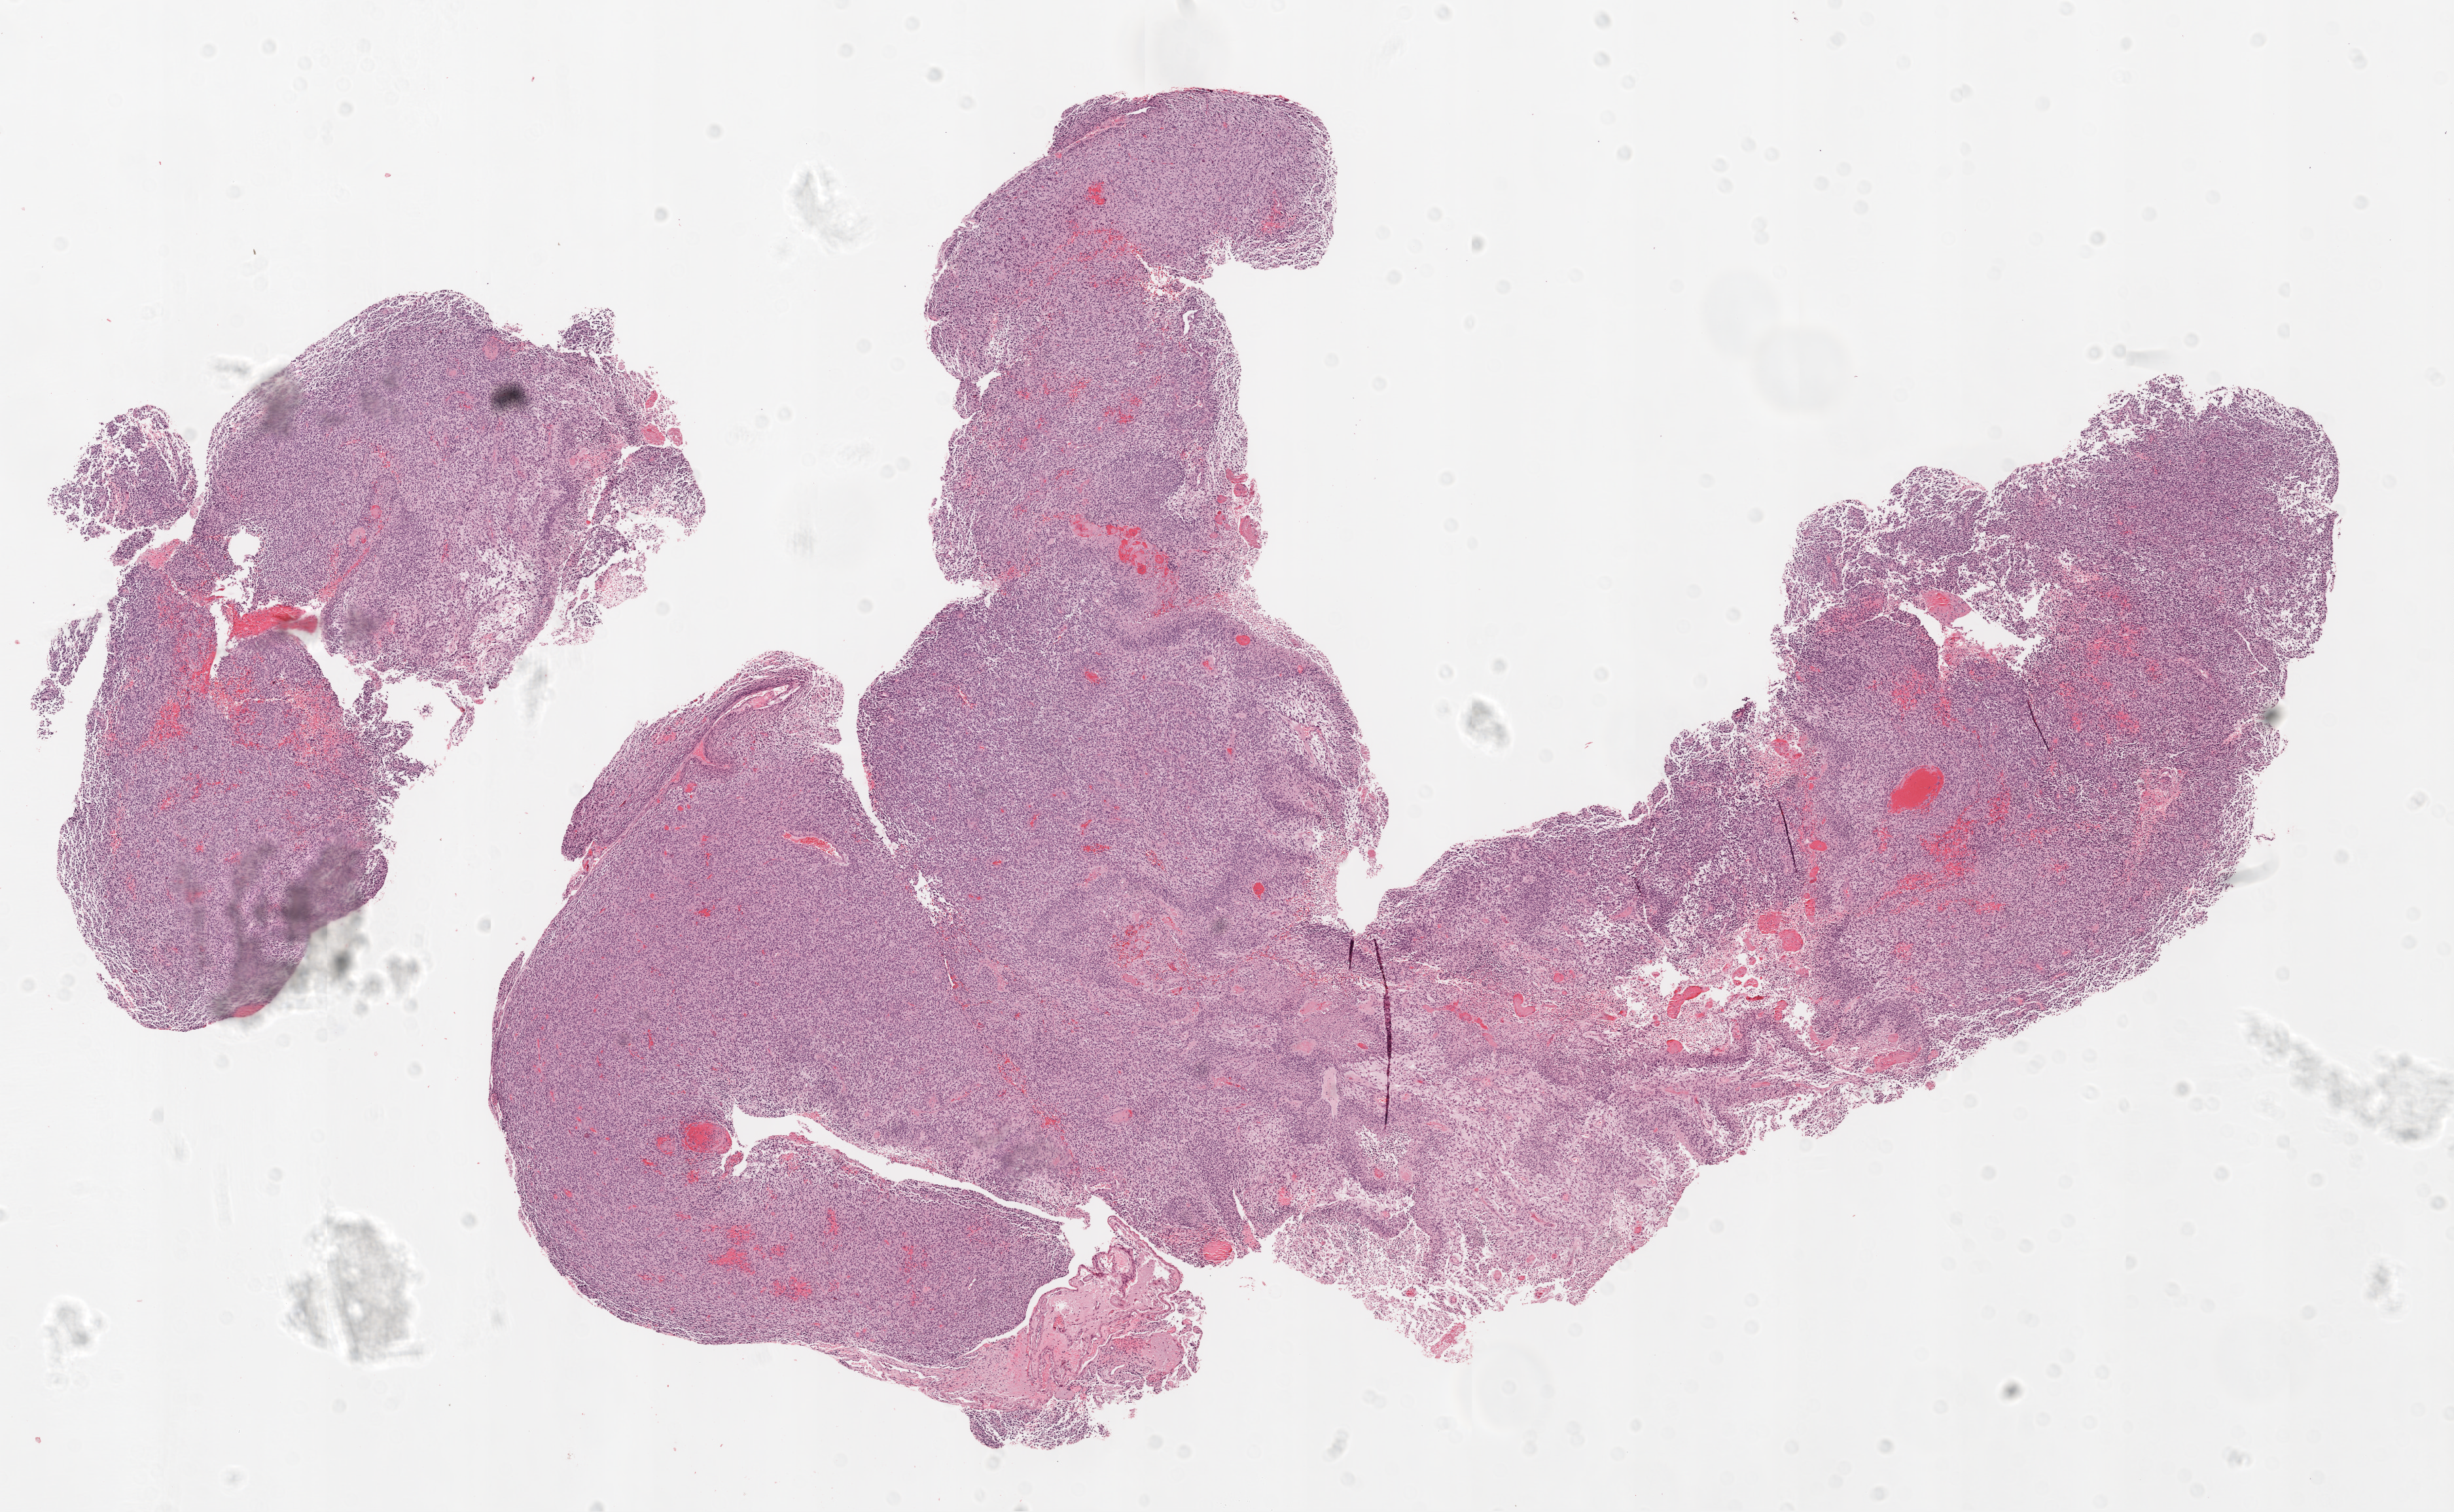
Digitized Hematoxylin and eosin (H&E) stained tissue section (whole slide) — whole scanned area (about 15.0 x 9.3 mm) shown as a low-resolution overview, formalin-fixed paraffin-embedded (FFPE) diagnostic section, brain, primary tumour sample. Male patient; age at initial diagnosis 65 years.
Diagnosis: Glioblastoma.